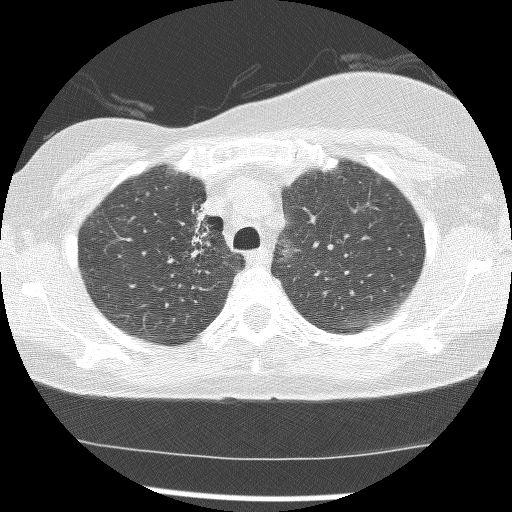
Chest CT (low-dose screening protocol), one axial image; baseline screening round; lung window (W 1500 / L -600 HU); 2.5 mm slice thickness; slice 37 of 172 in the series; 512 × 512 image matrix, field of view 315 × 315 mm. Female participant, aged 56 years at enrolment. Current smoker at enrolment.
Expert-annotated lung lesion, bounding box <165,198,223,274> (left, top, right, bottom; pixels). The screening reader recorded 2 non-calcified nodules or masses ≥4 mm on this exam; which of them this box marks is not recorded. Official screen result: positive, change unspecified: nodule(s) >= 4 mm or enlarging nodule(s), mass(es), or other non-specific abnormalities suspicious for lung cancer.